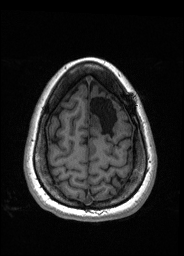
Pre-operative brain MRI before brain-tumour surgery, one axial slice. Position 43 of 176 along the scan axis. T1-weighted post-contrast. 1 mm slice thickness. 184 × 256 image matrix. Case-level facts recorded for this patient, not image findings: histopathology: Oligodendroglioma; WHO grade: 2; IDH mutation: yes; tumour location: Left Frontal.
Annotated regions visible in this slice (expert manual segmentation):
- tumour: bounding box (x1, y1, x2, y2) in pixels: (89, 114, 101, 126)